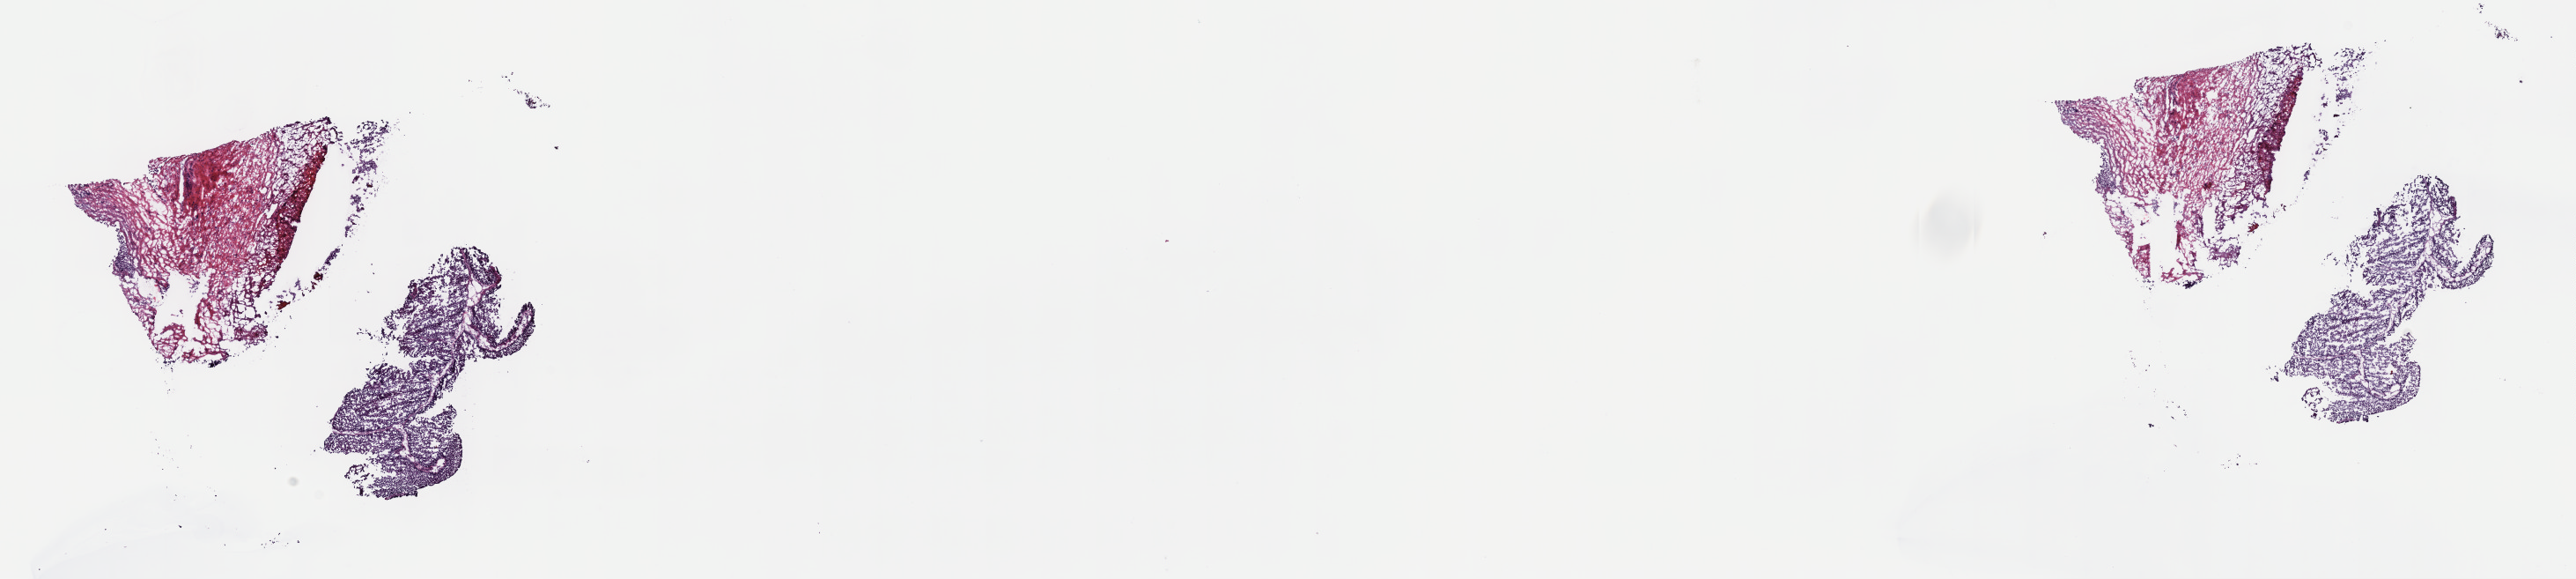
Whole-slide histology image, Hematoxylin and eosin (H&E) stained — whole scanned area (about 23.7 x 5.3 mm) shown as a low-resolution overview. Frozen section from the top of the tissue portion. Sample: primary tumour, bladder. Patient: male, age at initial diagnosis 85 years. Histologic grade: low grade. Slide review estimates, as recorded: tumour cells 70%, tumour nuclei 70%, normal cells 0%, stromal cells 30%, necrosis 0%. Inflammatory infiltration, as recorded: lymphocyte infiltration 0%, monocyte infiltration 0%, neutrophil infiltration 0%.
Histologic diagnosis: Papillary transitional cell carcinoma. AJCC pathologic stage: II (6th edition).